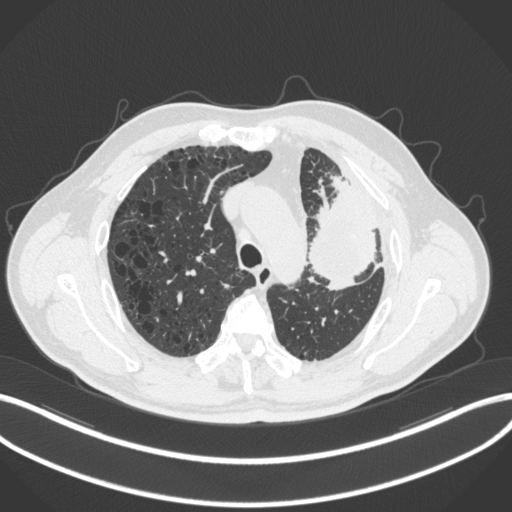
Chest CT, one axial slice. Position 221 of 286 along the scan axis. Reconstruction kernel B31f. 120 kVp. Lung window (W 1500 / L -600 HU). 1 mm slice thickness. 512 × 512 image matrix. Patient: male, 68 years. From the clinical record (not read from this slice): clinical TNM (as recorded): T3 N3 M1.
Outlined on this slice (bounding box drawn by a radiologist):
- lung tumour (recorded histology: adenocarcinoma): box from (x=307, y=170) to (x=382, y=297) px